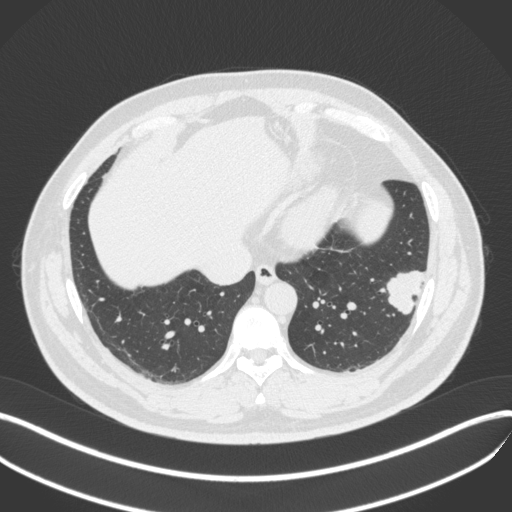
Chest CT, one axial slice; reconstruction kernel B31f; 120 kVp; lung window (W 1500 / L -600 HU); 1 mm slice thickness; 512 × 512 image matrix. Patient: male, 39 years. From the clinical record (not read from this slice): clinical TNM (as recorded): T2a N0 M0; histopathological grade: G2-3.
Outlined on this slice (bounding box drawn by a radiologist):
- lung tumour (recorded histology: adenocarcinoma): bounding box [x1, y1, x2, y2] px = [377, 264, 430, 324]